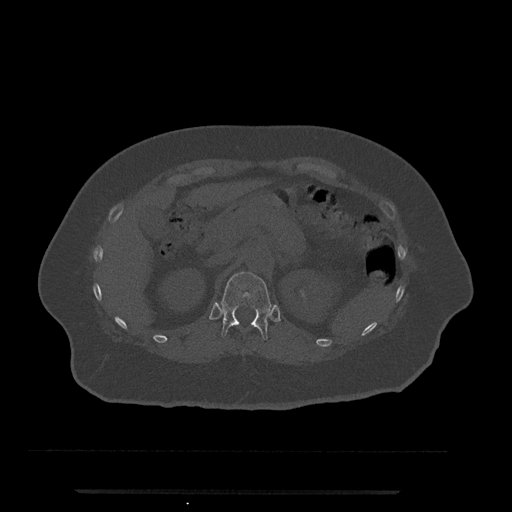
CT including the spine, one axial slice. Position 178 of 797 along the scan axis. Reconstruction kernel Br40s/3. Bone window (W 1800 / L 400 HU). 0.5 mm slice thickness. 512 × 512 image matrix, field of view 440 × 440 mm. Patient: female, 51 years. Case-level facts recorded for this patient, not image findings: primary cancer: neuro; vertebrae with lytic lesions (as recorded): T8.
Outlined on this slice (semi-automatic segmentation, software-assisted and operator-edited):
- T12 vertebra: box from (x=221, y=272) to (x=272, y=341) px